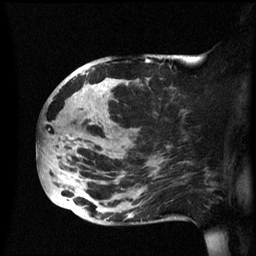
Breast MRI (dynamic contrast-enhanced), one sagittal slice. Position 27 of 60 along the scan axis. Dynamic contrast-enhanced series, image 2 of 3 at this slice position (ordered by acquisition). 1.5 T. TE 4.2 ms, TR 8.4 ms. 2.4 mm slice thickness. 256 × 256 image matrix, field of view 230 × 230 mm. Patient: female, 49 years.
Structures marked on this image (semi-automatically segmented with operator editing):
- analysis volume of interest (the breast-tissue region the enhancement analysis was run in; not a lesion): bounding box [x1, y1, x2, y2] px = [39, 55, 174, 225]
- tumour enhancement mask (voxels above the 70 % enhancement threshold inside the analysis volume of interest): [44, 73, 104, 211]